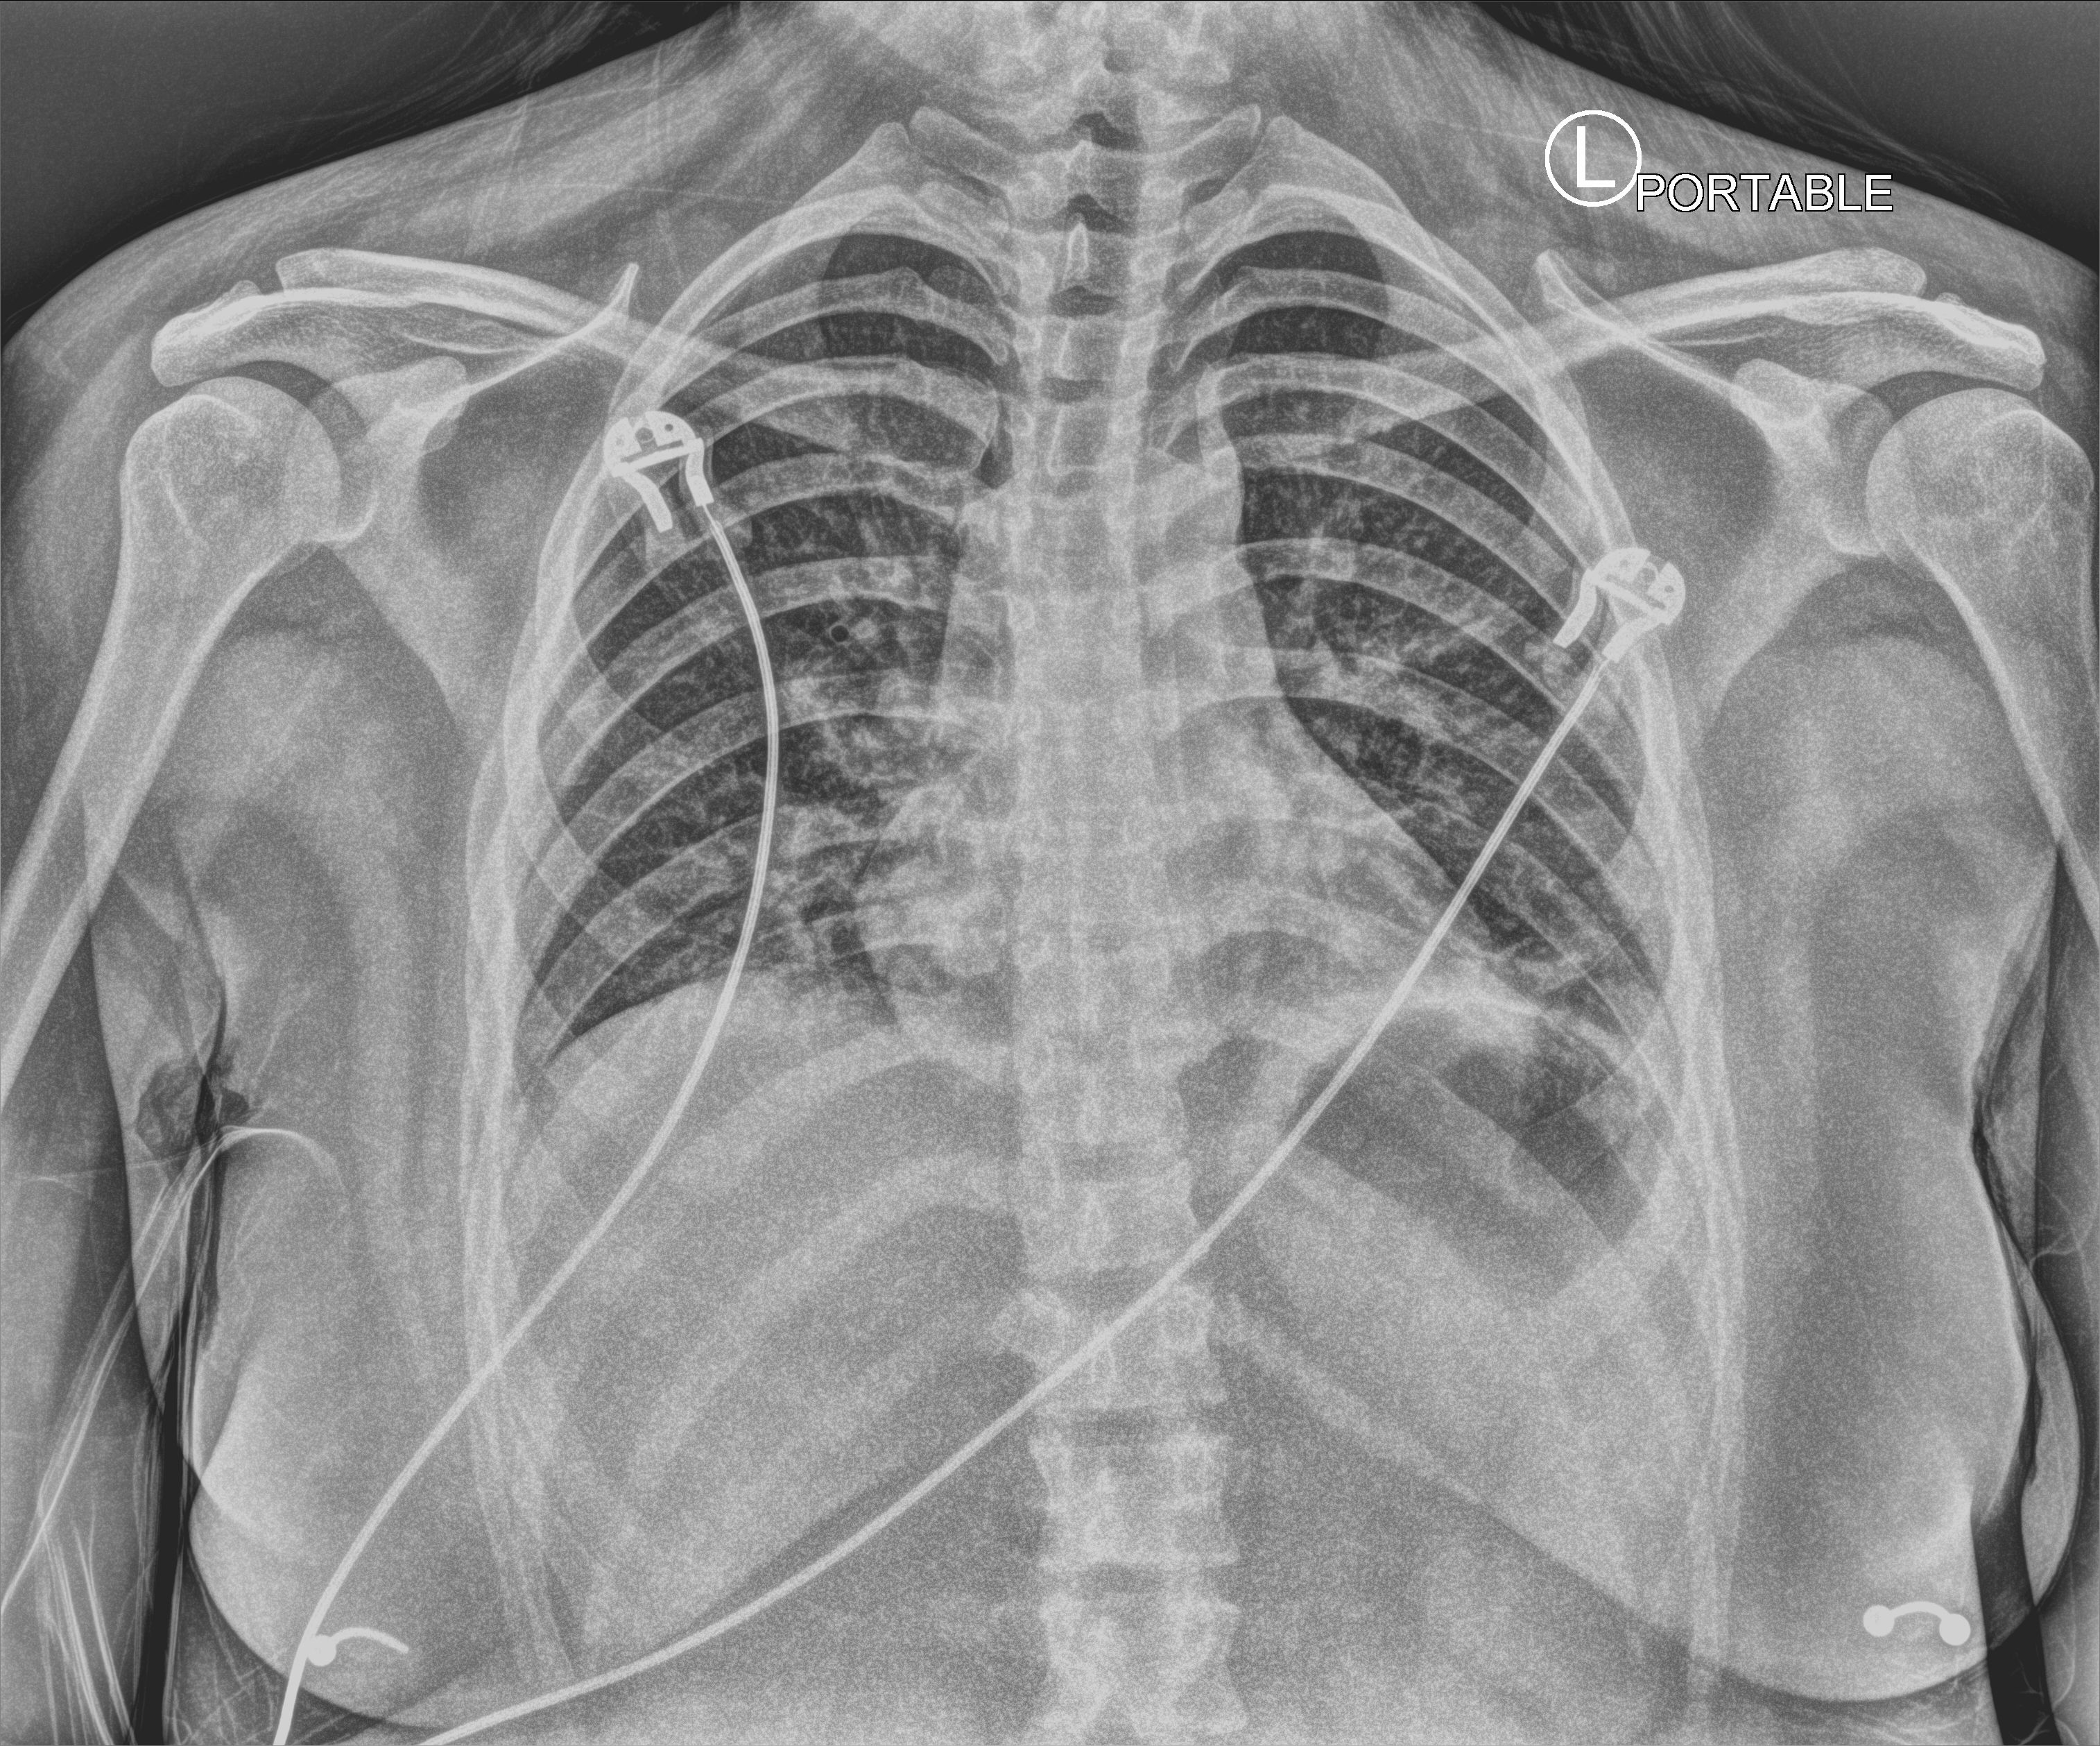
Bedside chest radiograph (computed radiography); anteroposterior (AP) projection. Patient hospitalised with COVID-19; female, aged 18–59 years.
From the hospital-stay record, not from the radiograph (when in the stay this image was taken is not recorded):
- other chronic lung disease (admission record): no